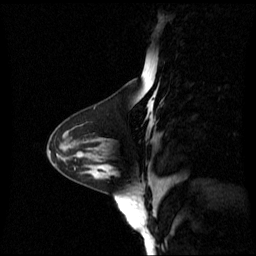
Breast MRI (dynamic contrast-enhanced), one sagittal slice; position 24 of 60 along the scan axis; dynamic contrast-enhanced series, image 2 of 3 at this slice position (ordered by acquisition); 1.5 T; TE 4.2 ms, TR 8.4 ms; 2.4 mm slice thickness; 256 × 256 image matrix, field of view 250 × 250 mm. Female patient, age 44 years. From the clinical record (not read from this slice): setting: breast cancer imaged before/during neoadjuvant chemotherapy; receptor status: triple-negative.
Annotated regions visible in this slice (semi-automatically segmented with operator editing):
- analysis volume of interest (the breast-tissue region the enhancement analysis was run in; not a lesion): box from (x=79, y=148) to (x=132, y=190) px
- tumour enhancement mask (voxels above the 70 % enhancement threshold inside the analysis volume of interest): (x=110, y=168)–(x=112, y=170)